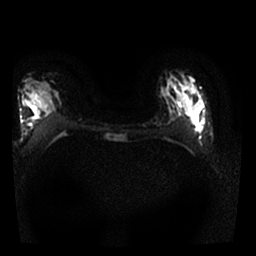
Breast MRI, one axial slice; slice 15 of 25 in the series (ordered by position); diffusion-weighted series; image 2 of 4 stored at this slice position (different b-values; order by instance number); 1.5 T; 256 × 256 image matrix, field of view 300 × 300 mm. Female patient.
Structures marked on this image (manually delineated by an expert):
- tumour on diffusion-weighted imaging: bounding box [x1, y1, x2, y2] px = [193, 116, 201, 132]